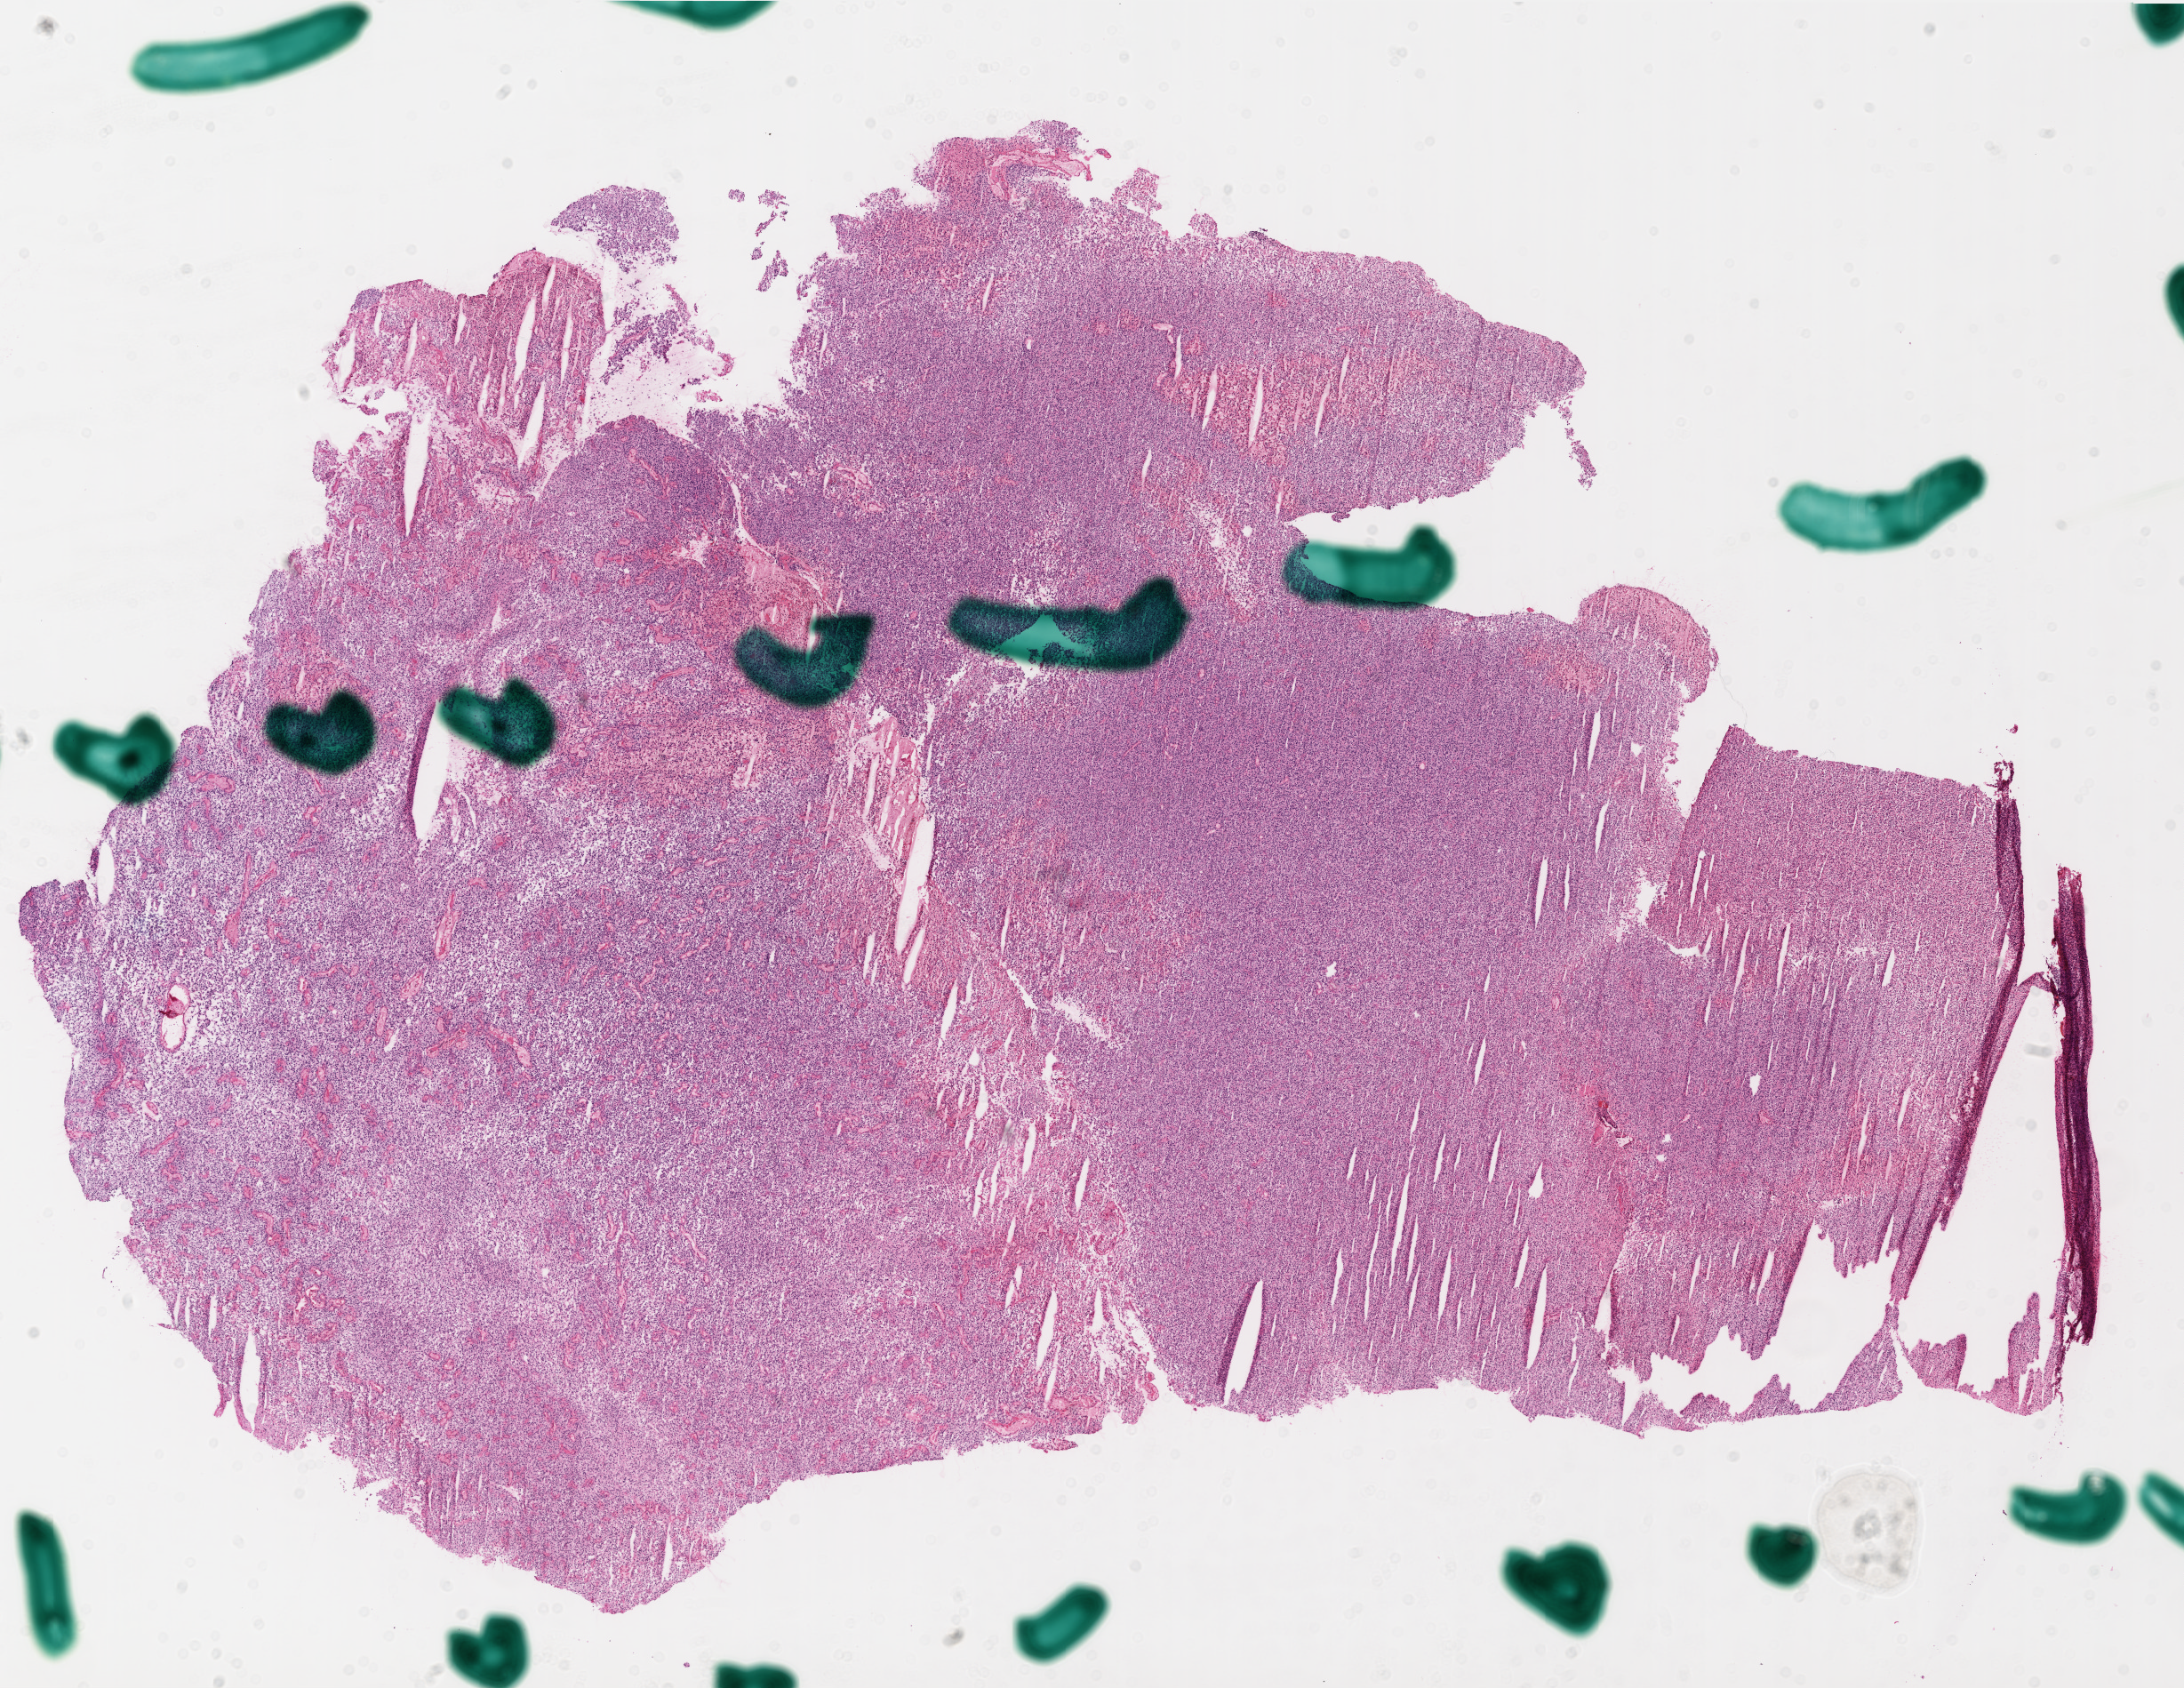
H&E-stained whole-slide image — whole scanned area (about 19.8 x 15.3 mm, acquisition: 20x scan) shown as a low-resolution overview. Frozen section from the top of the tissue portion. Sample: primary tumour, brain. Female patient; age at initial diagnosis 43 years. Slide review estimates, as recorded: tumour cells 90%, tumour nuclei 100%, normal cells 0%, stromal cells 0%, necrosis 10%.
• diagnosis: Glioblastoma